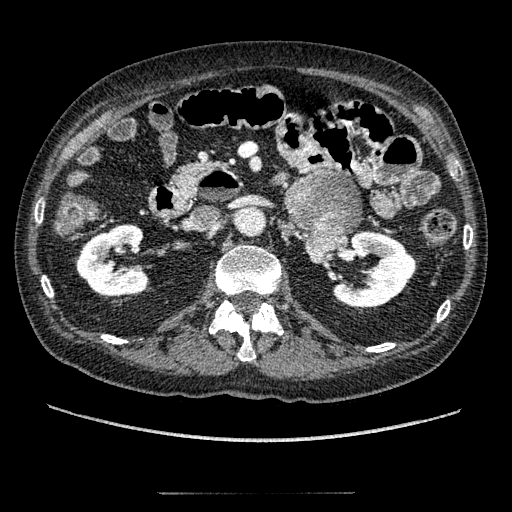
Contrast-enhanced abdominal CT, one axial slice; position 96 of 274 along the scan axis; reconstruction kernel STANDARD; 120 kVp; intravenous contrast given; soft-tissue window (W 400 / L 40 HU); 1.25 mm slice thickness; 512 × 512 image matrix, field of view 381 × 381 mm. Patient: male, 69 years. From the clinical record (not read from this slice): diagnosis: adrenocortical carcinoma; tumour side: left adrenal; tumour size at pathology: 6.1 cm; Ki-67 index: 10 %; stage (as recorded): 3.
Annotated regions visible in this slice (semi-automatic segmentation, software-assisted and operator-edited):
- mass: bounding box (x1, y1, x2, y2) in pixels: (288, 172, 360, 260)